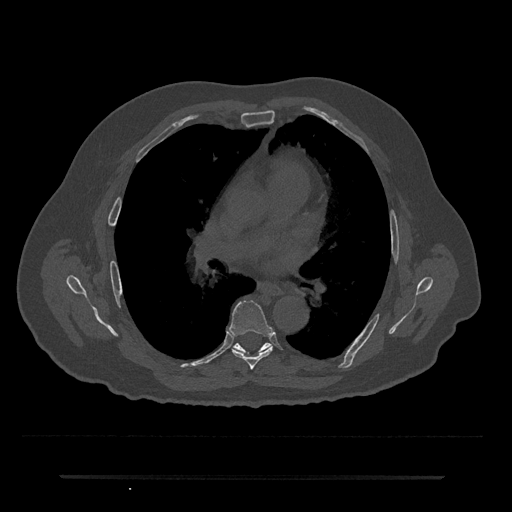
CT including the spine, one axial slice. Slice 421 of 797 in the series (ordered by position). Reconstruction kernel Br40s/3. Bone window (W 1800 / L 400 HU). 512 × 512 image matrix, field of view 437 × 437 mm. Patient: male, 69 years. From the clinical record (not read from this slice): primary cancer: prostate.
Annotated regions visible in this slice (semi-automatic segmentation, software-assisted and operator-edited):
- T6 vertebra: bounding box [x1, y1, x2, y2] px = [229, 300, 274, 369]
- T7 vertebra: [233, 343, 271, 351]